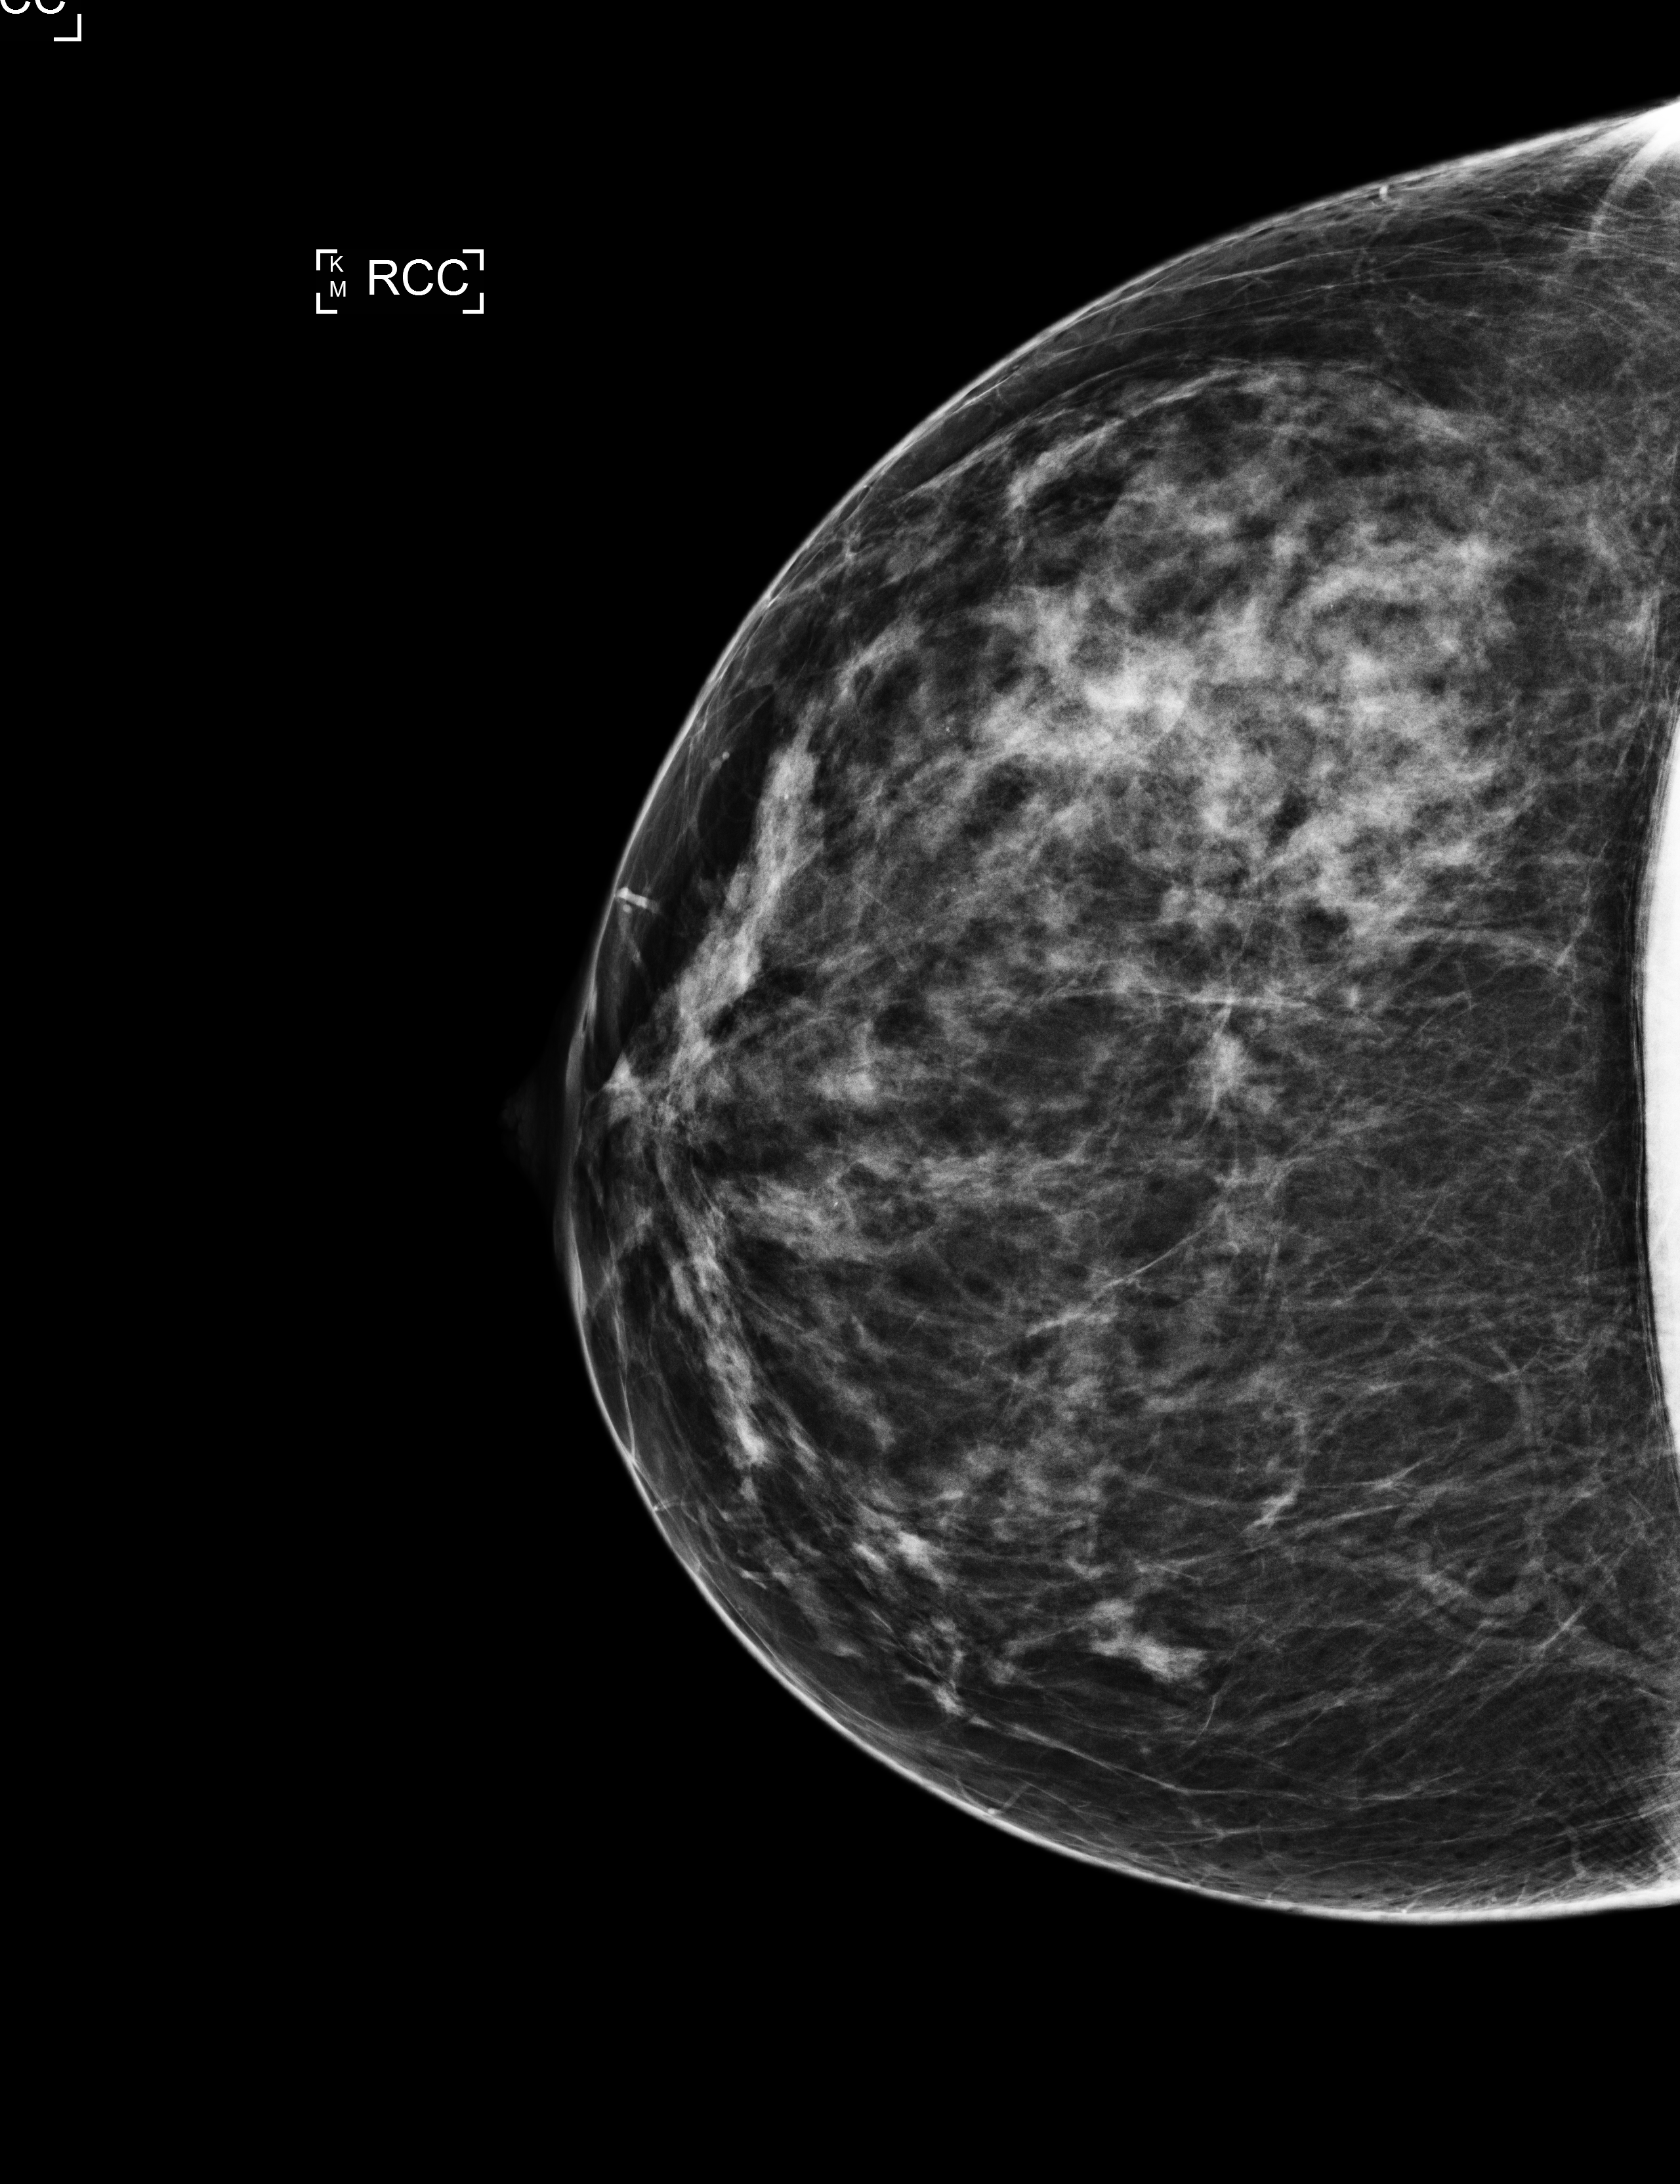
Annual screening mammography examination, system: Selenia Dimensions. Patient: female, 44 years.
Image type: full-field digital mammogram. Breast: right. Projection: craniocaudal (CC) view.